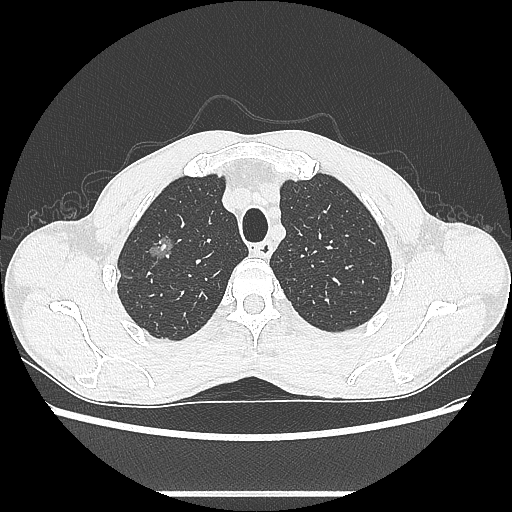
Chest CT, one axial slice; slice 493 of 601 in the series (ordered by position); reconstruction kernel LUNG; 100 kVp; lung window (W 1500 / L -600 HU); 0.62 mm slice thickness; 512 × 512 image matrix, field of view 357 × 357 mm. Patient: male, 54 years. From the clinical record (not read from this slice): clinical TNM (as recorded): T1a N0 M0.
Structures marked on this image (rectangle marked by the reading radiologist):
- lung tumour (recorded histology: adenocarcinoma): bounding box (x1, y1, x2, y2) in pixels: (146, 221, 180, 265)